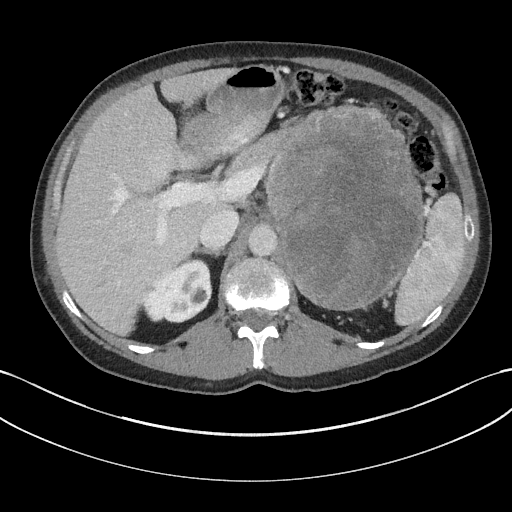
Contrast-enhanced abdominal CT, one axial slice. Position 114 of 147 along the scan axis. Reconstruction kernel I31f/3. Intravenous contrast given. Soft-tissue window (W 400 / L 40 HU). 3 mm slice thickness. 512 × 512 image matrix, field of view 384 × 384 mm. Patient: male, 58 years. From the clinical record (not read from this slice): diagnosis: adrenocortical carcinoma; tumour side: left adrenal; tumour size at pathology: 22 cm; Ki-67 index: 26 %; stage (as recorded): 2.
Outlined on this slice (semi-automatically segmented with operator editing):
- mass: bounding box <269,107,421,307> (left, top, right, bottom; pixels)